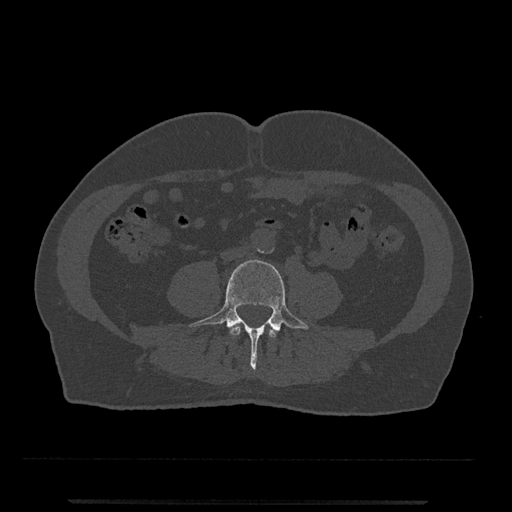
CT including the spine, one axial slice. Position 145 of 797 along the scan axis. 120 kVp. Bone window (W 1800 / L 400 HU). 0.5 mm slice thickness. 512 × 512 image matrix. Patient: male, 63 years. From the clinical record (not read from this slice): primary cancer: prostate.
Structures marked on this image (semi-automatically segmented with operator editing):
- L3 vertebra: bounding box <230,325,277,338> (left, top, right, bottom; pixels)
- L4 vertebra: <189,259,310,369>